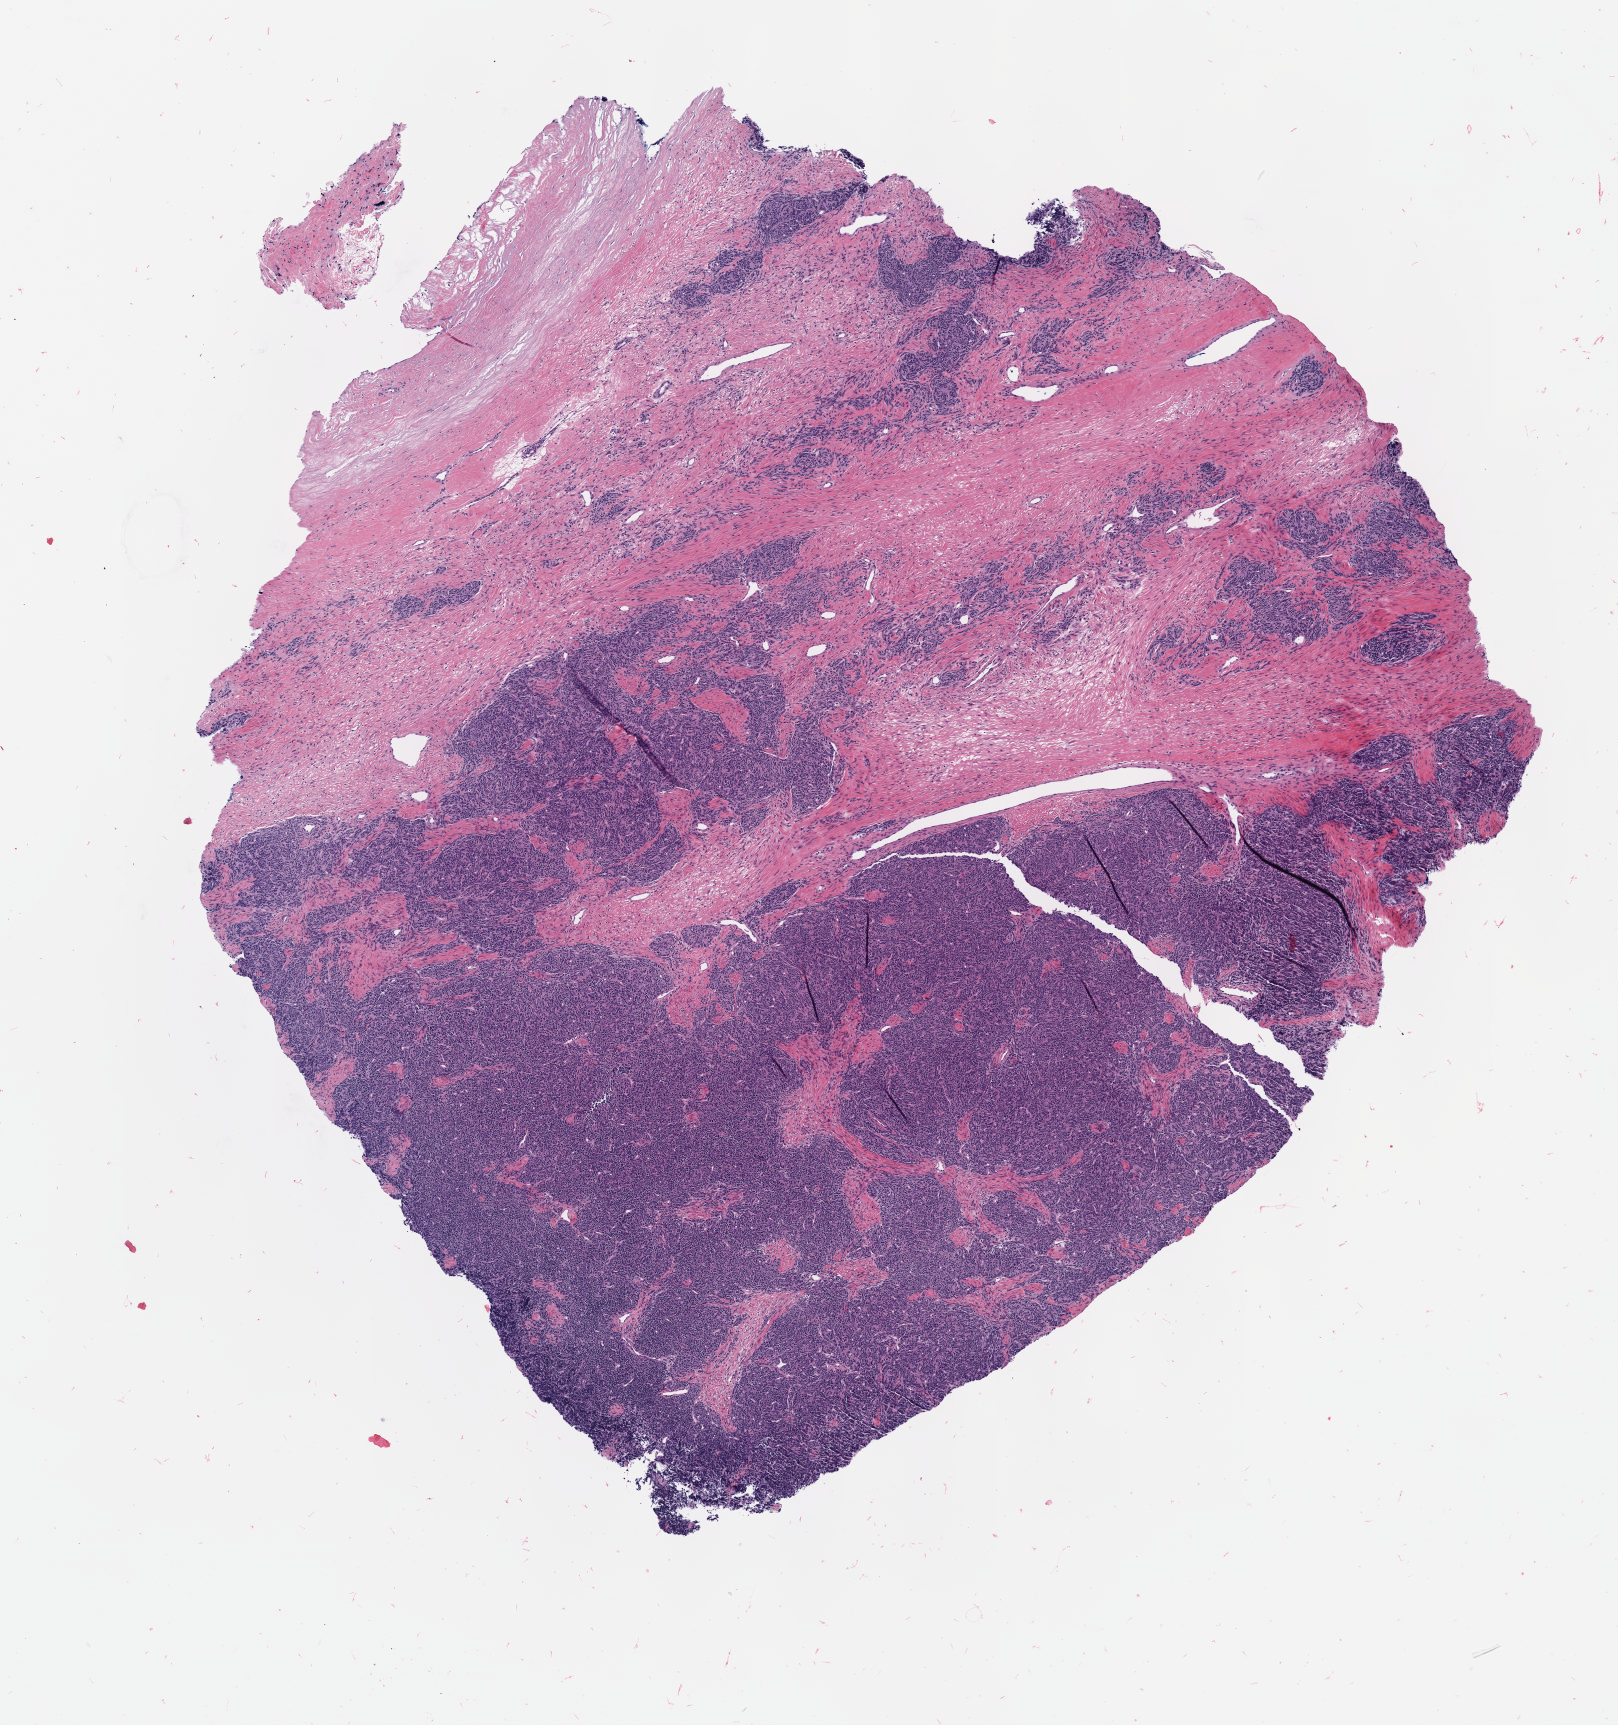
Digitized H&E tissue section (whole slide) — shown as a low-resolution overview of the whole scanned area (about 6.5 x 7.0 mm); formalin-fixed paraffin-embedded (FFPE) diagnostic section; sample: primary tumour, thymus. Patient: male, age at initial diagnosis 53 years.
• diagnosis: Thymoma, type AB, malignant